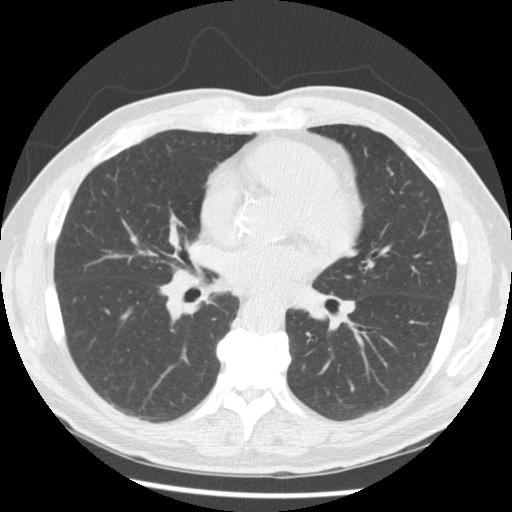
Chest CT (low-dose screening protocol), one axial image. First (baseline) screen. Lung window (W 1500 / L -600 HU). 2.5 mm slice thickness. Standard (soft-tissue) reconstruction kernel (STANDARD). Slice 81 of 166 in the series. Male, age 62 years at enrolment. Current smoker at enrolment.
Expert-annotated lung lesion, bounding box (x1, y1, x2, y2) in pixels: (155, 250, 217, 309). No non-calcified nodule or mass ≥4 mm was recorded by the screening reader at this exam. Official screen result: negative screen, minor abnormalities not suspicious for lung cancer. Participant outcome: lung cancer diagnosed 146 days after this screen — small cell carcinoma, NOS, right hilum, mediastinum, poorly differentiated (G3), stage IV (AJCC 6th edition).